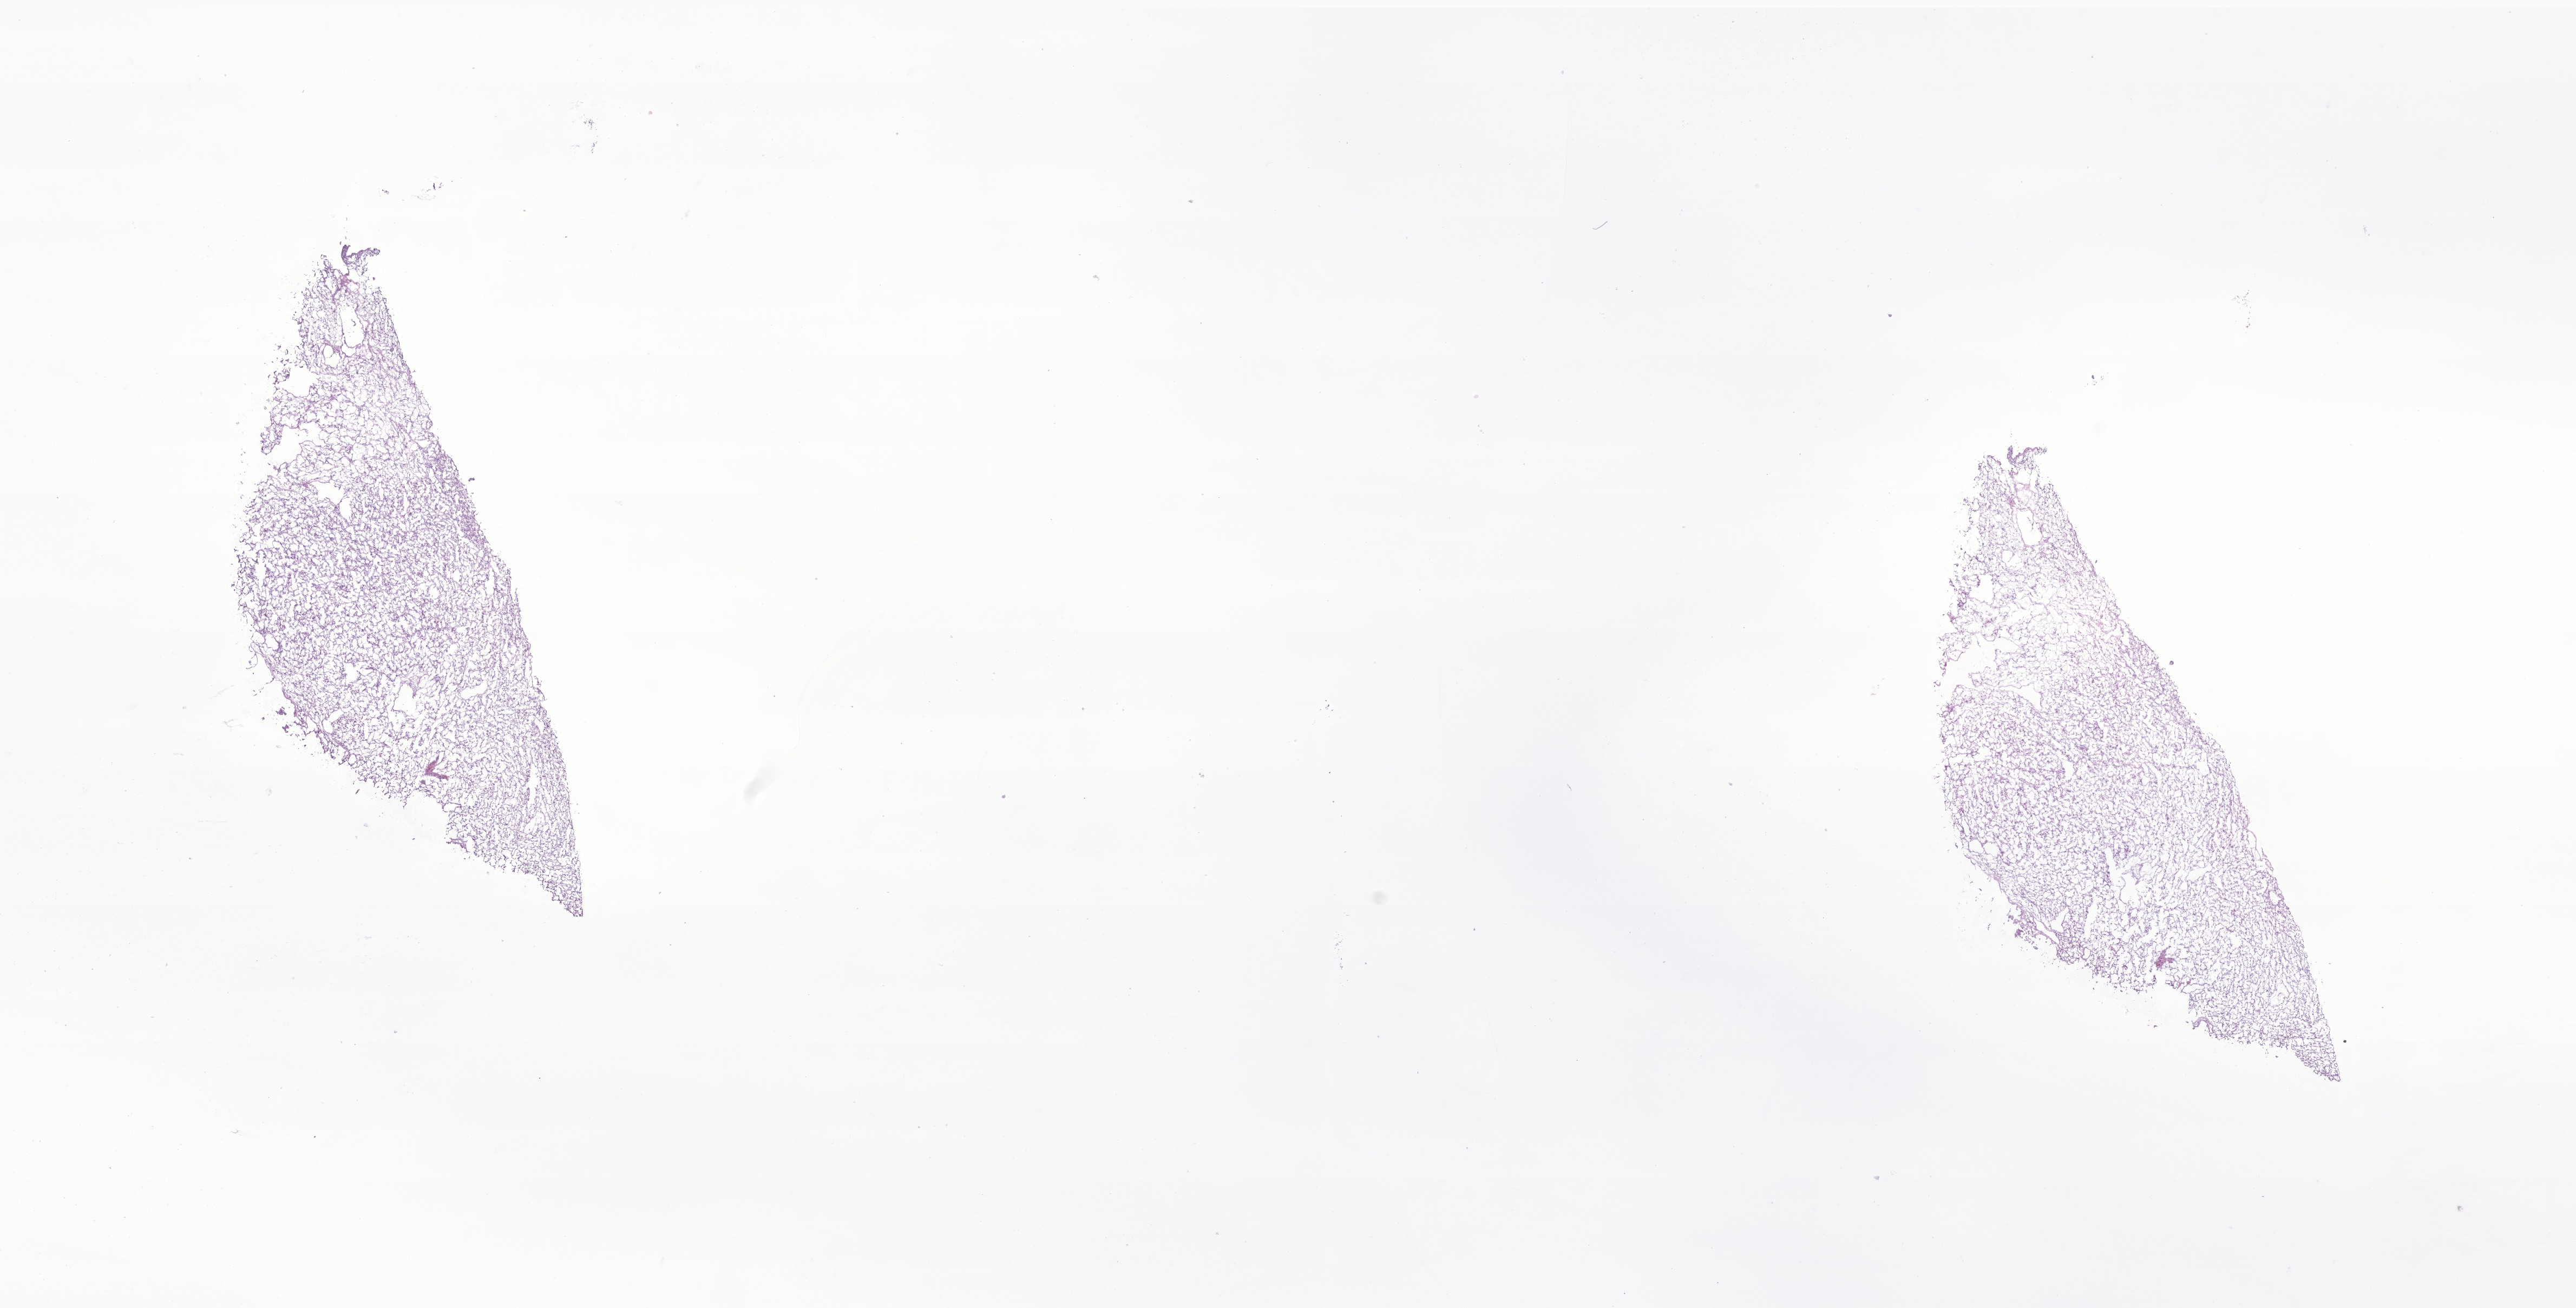
Digitized haematoxylin and eosin-stained section of tumor tissue from the brain, shown as a low-resolution overview of the whole scanned area (about 20.1 x 10.2 mm), frozen section (OCT-embedded). Patient: male, age 177 months (14 years 9 months).
- recorded diagnosis: Neoplasm, uncertain whether benign or malignant